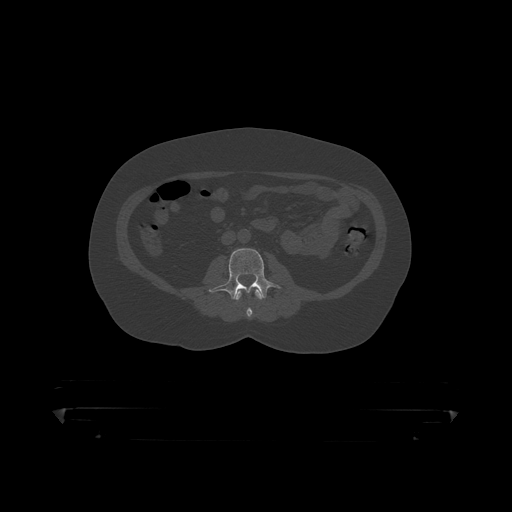
CT including the spine, one axial slice; position 95 of 390 along the scan axis; reconstruction kernel STANDARD; 120 kVp; bone window (W 1800 / L 400 HU); 1.25 mm slice thickness; 512 × 512 image matrix. Male patient, age 60 years. Case-level facts recorded for this patient, not image findings: primary cancer: prostate.
Outlined on this slice (semi-automatic segmentation, software-assisted and operator-edited):
- L2 vertebra: box from (x=236, y=289) to (x=264, y=319) px
- L3 vertebra: (x=208, y=249)–(x=280, y=301)